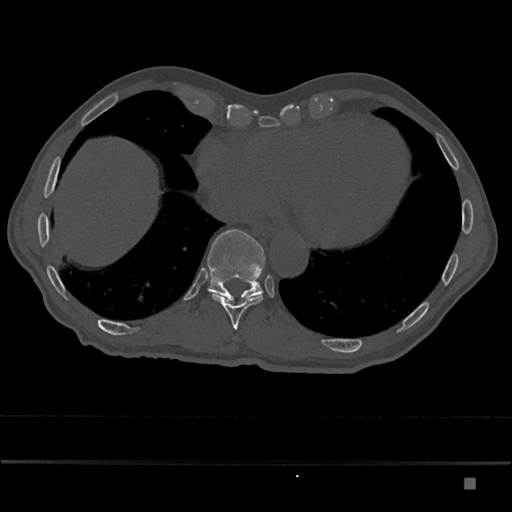
CT including the spine, one axial slice; slice 717 of 797 in the series (ordered by position); reconstruction kernel Br40s/3; bone window (W 1800 / L 400 HU); 512 × 512 image matrix, field of view 390 × 390 mm. Male patient, age 72 years. From the clinical record (not read from this slice): primary cancer: prostate.
Annotated regions visible in this slice (semi-automatic segmentation, software-assisted and operator-edited):
- T10 vertebra: box from (x=212, y=293) to (x=263, y=330) px
- T11 vertebra: (x=207, y=229)–(x=265, y=303)